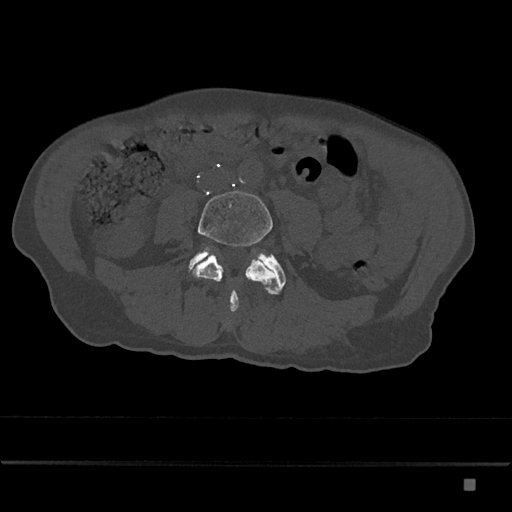
CT including the spine, one axial slice. Position 322 of 797 along the scan axis. Bone window (W 1800 / L 400 HU). 0.5 mm slice thickness. 512 × 512 image matrix, field of view 390 × 390 mm. Male patient, age 72 years. Case-level facts recorded for this patient, not image findings: primary cancer: prostate.
Outlined on this slice (semi-automatically segmented with operator editing):
- L4 vertebra: bounding box (x1, y1, x2, y2) in pixels: (190, 191, 277, 312)
- L5 vertebra: (189, 247, 286, 294)